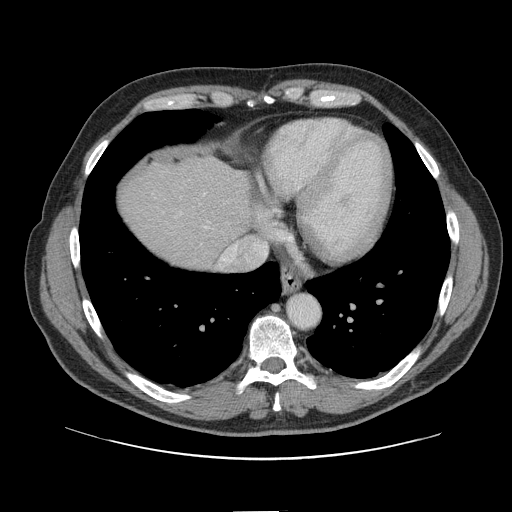
Contrast-enhanced abdominal CT, one axial slice; slice 135 of 161 in the series (ordered by position); 120 kVp; intravenous contrast given; soft-tissue window (W 400 / L 40 HU); 2.5 mm slice thickness; 512 × 512 image matrix, field of view 412 × 412 mm. Male patient, age 66 years. Case-level facts recorded for this patient, not image findings: diagnosis: colorectal cancer liver metastases, imaged before liver resection; multiple liver metastases: no; largest metastasis: 3.5 cm; chemotherapy before resection: yes.
Outlined on this slice (manually delineated by an expert):
- hepatic veins: bounding box <204,194,240,268> (left, top, right, bottom; pixels)
- liver: <121,162,250,268>
- planned liver remnant (the part of the liver to remain after resection): <121,162,250,268>